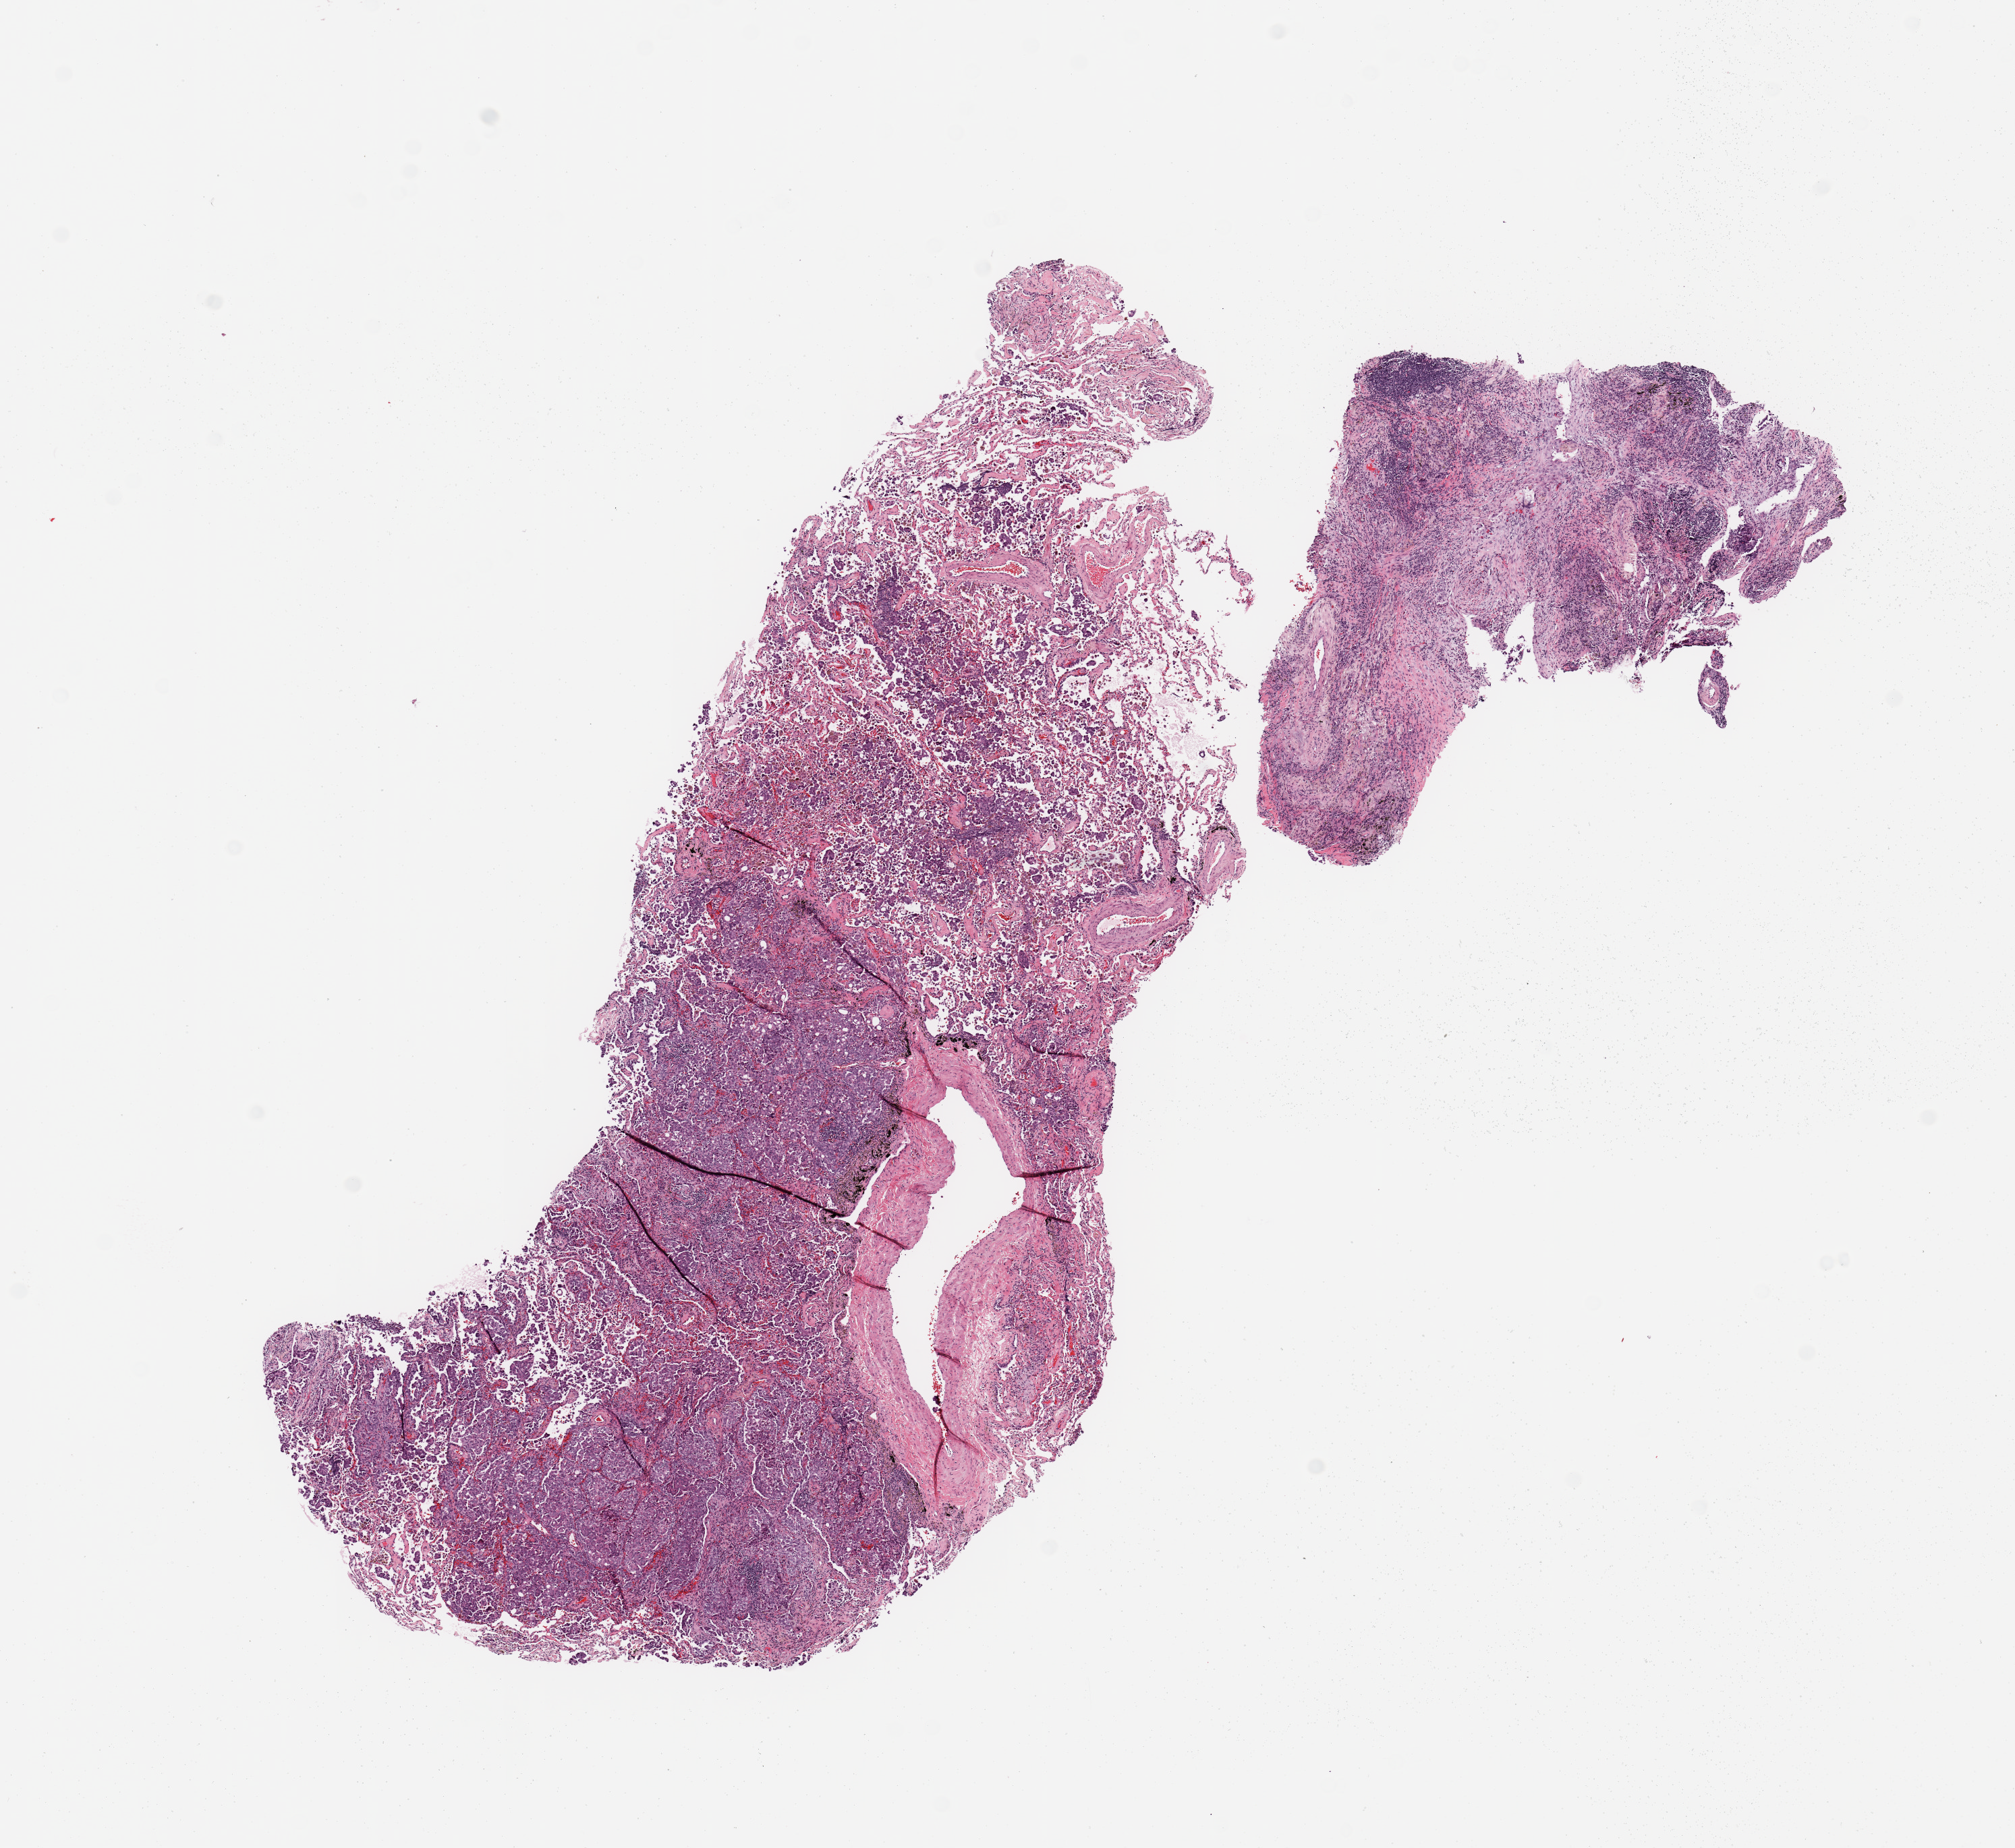
Digitized Hematoxylin and eosin (H&E) stained tissue section (whole slide) — shown as a low-resolution overview of the whole scanned area (about 11.8 x 10.8 mm, acquisition: 20x scan); lung, tumour tissue. 62-year-old male patient.
Histologic diagnosis: Adenocarcinoma, NOS.